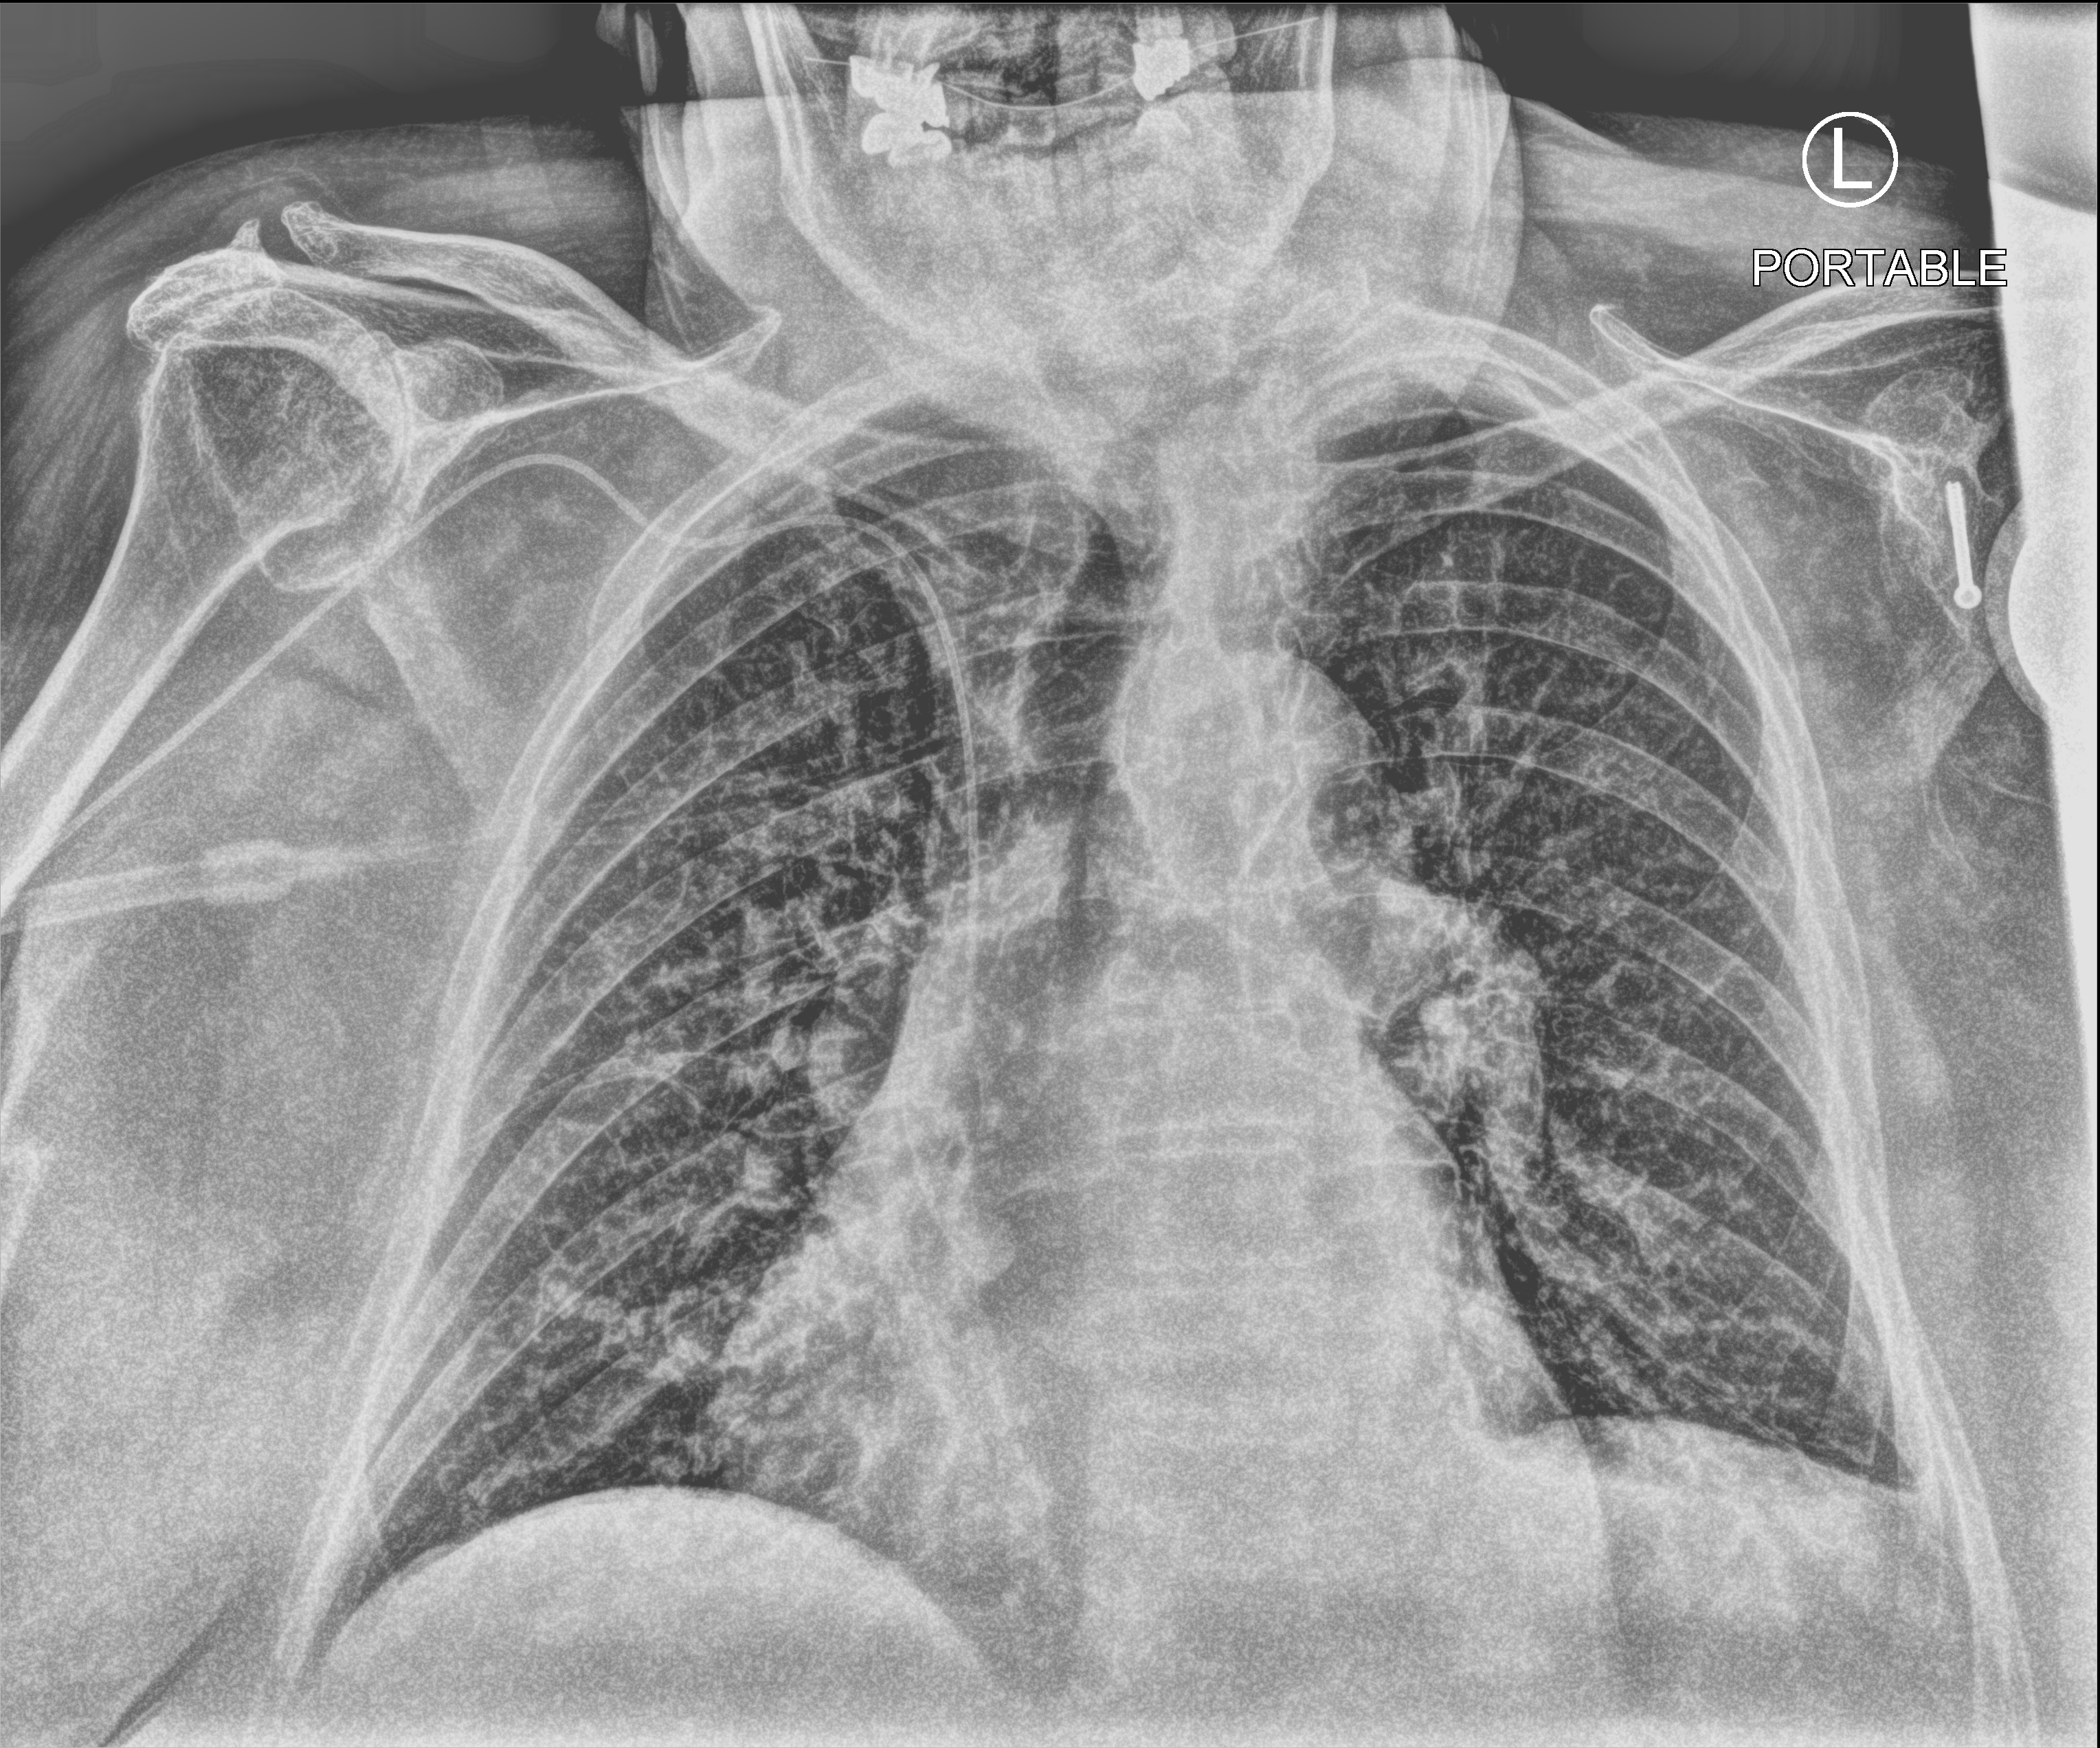
Portable chest radiograph; anteroposterior (AP) projection. Female patient hospitalised with COVID-19, age 75–90 years.
Hospital-stay facts (about this admission, not read from this image; timing relative to this image not recorded): admitted to intensive care during this hospital stay: no; mechanically ventilated during this hospital stay: no; length of hospital stay: 7 days.